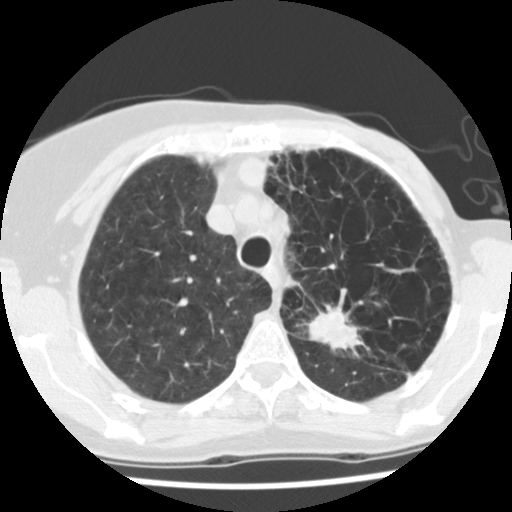
Low-dose screening chest CT, one axial slice; slice 100 of 128 in the series (ordered by position); reconstruction kernel STANDARD; lung window (W 1500 / L -600 HU); 2.5 mm slice thickness; 512 × 512 image matrix.
Outlined on this slice (outlined manually by an expert reader):
- lesion 1 (tumor, upper lobe of left lung): box from (x=307, y=304) to (x=364, y=356) px